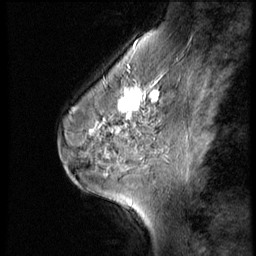
Breast MRI (dynamic contrast-enhanced), one sagittal slice. Slice 39 of 56 in the series (ordered by position). 3 images stored at this slice position (order not interpretable as contrast timing). 1.5 T. TE 4.2 ms, TR 9 ms. 2.5 mm slice thickness. 256 × 256 image matrix, field of view 180 × 180 mm. Patient: female, 45 years. From the clinical record (not read from this slice): setting: breast cancer imaged before/during neoadjuvant chemotherapy; receptor status: HR-positive, HER2-negative.
Annotated regions visible in this slice (semi-automatic segmentation, software-assisted and operator-edited):
- analysis volume of interest (the breast-tissue region the enhancement analysis was run in; not a lesion): bounding box <102,77,166,129> (left, top, right, bottom; pixels)
- tumour enhancement mask (voxels above the 140 % enhancement threshold inside the analysis volume of interest): <102,77,161,129>